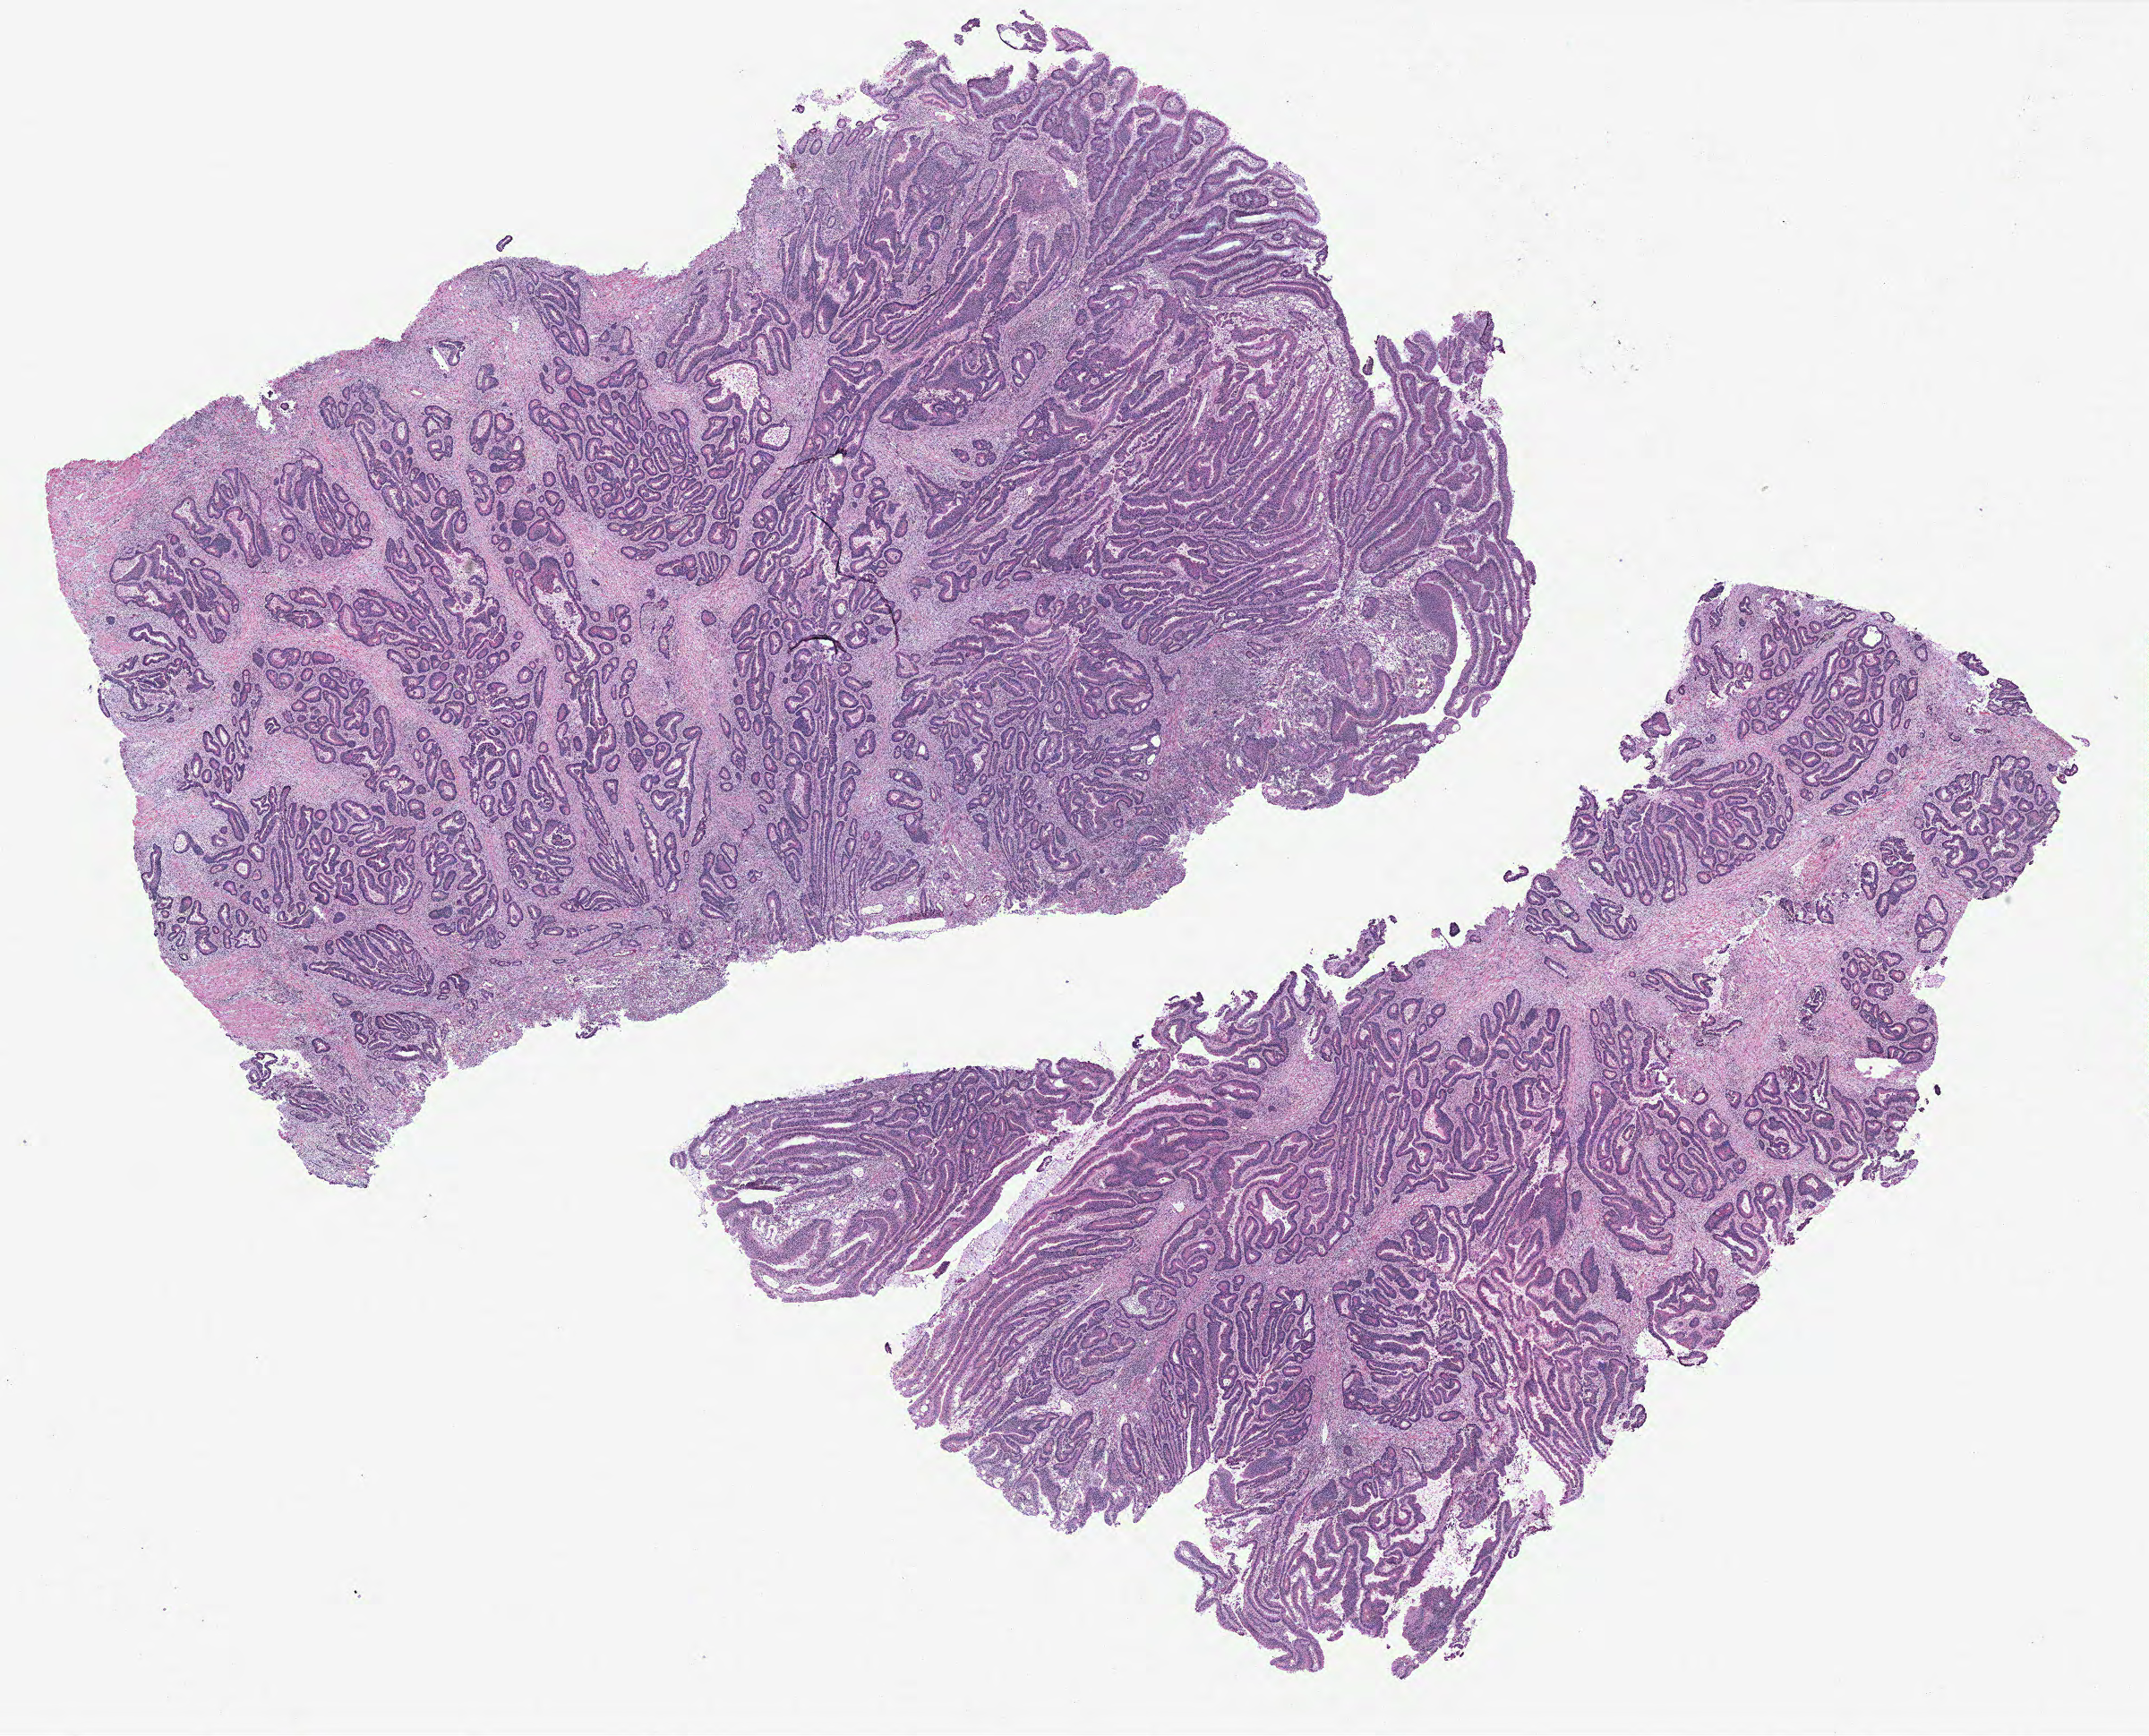
H&E-stained whole-slide image — shown as a low-resolution overview of the whole scanned area (about 19.2 x 15.5 mm, from a 40x scan); normal (non-tumour) tissue sample, colon. 66-year-old male patient.
• this section: normal (non-tumour) tissue from the same patient
• patient diagnosis: Adenocarcinoma, NOS